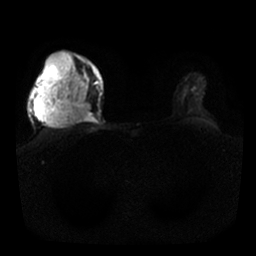
Breast MRI, one axial slice. Position 20 of 25 along the scan axis. Diffusion-weighted series; image 2 of 4 stored at this slice position (different b-values; order by instance number). 1.5 T. 256 × 256 image matrix. Female patient.
Outlined on this slice (outlined manually by an expert reader):
- tumour on diffusion-weighted imaging: box from (x=36, y=54) to (x=93, y=128) px